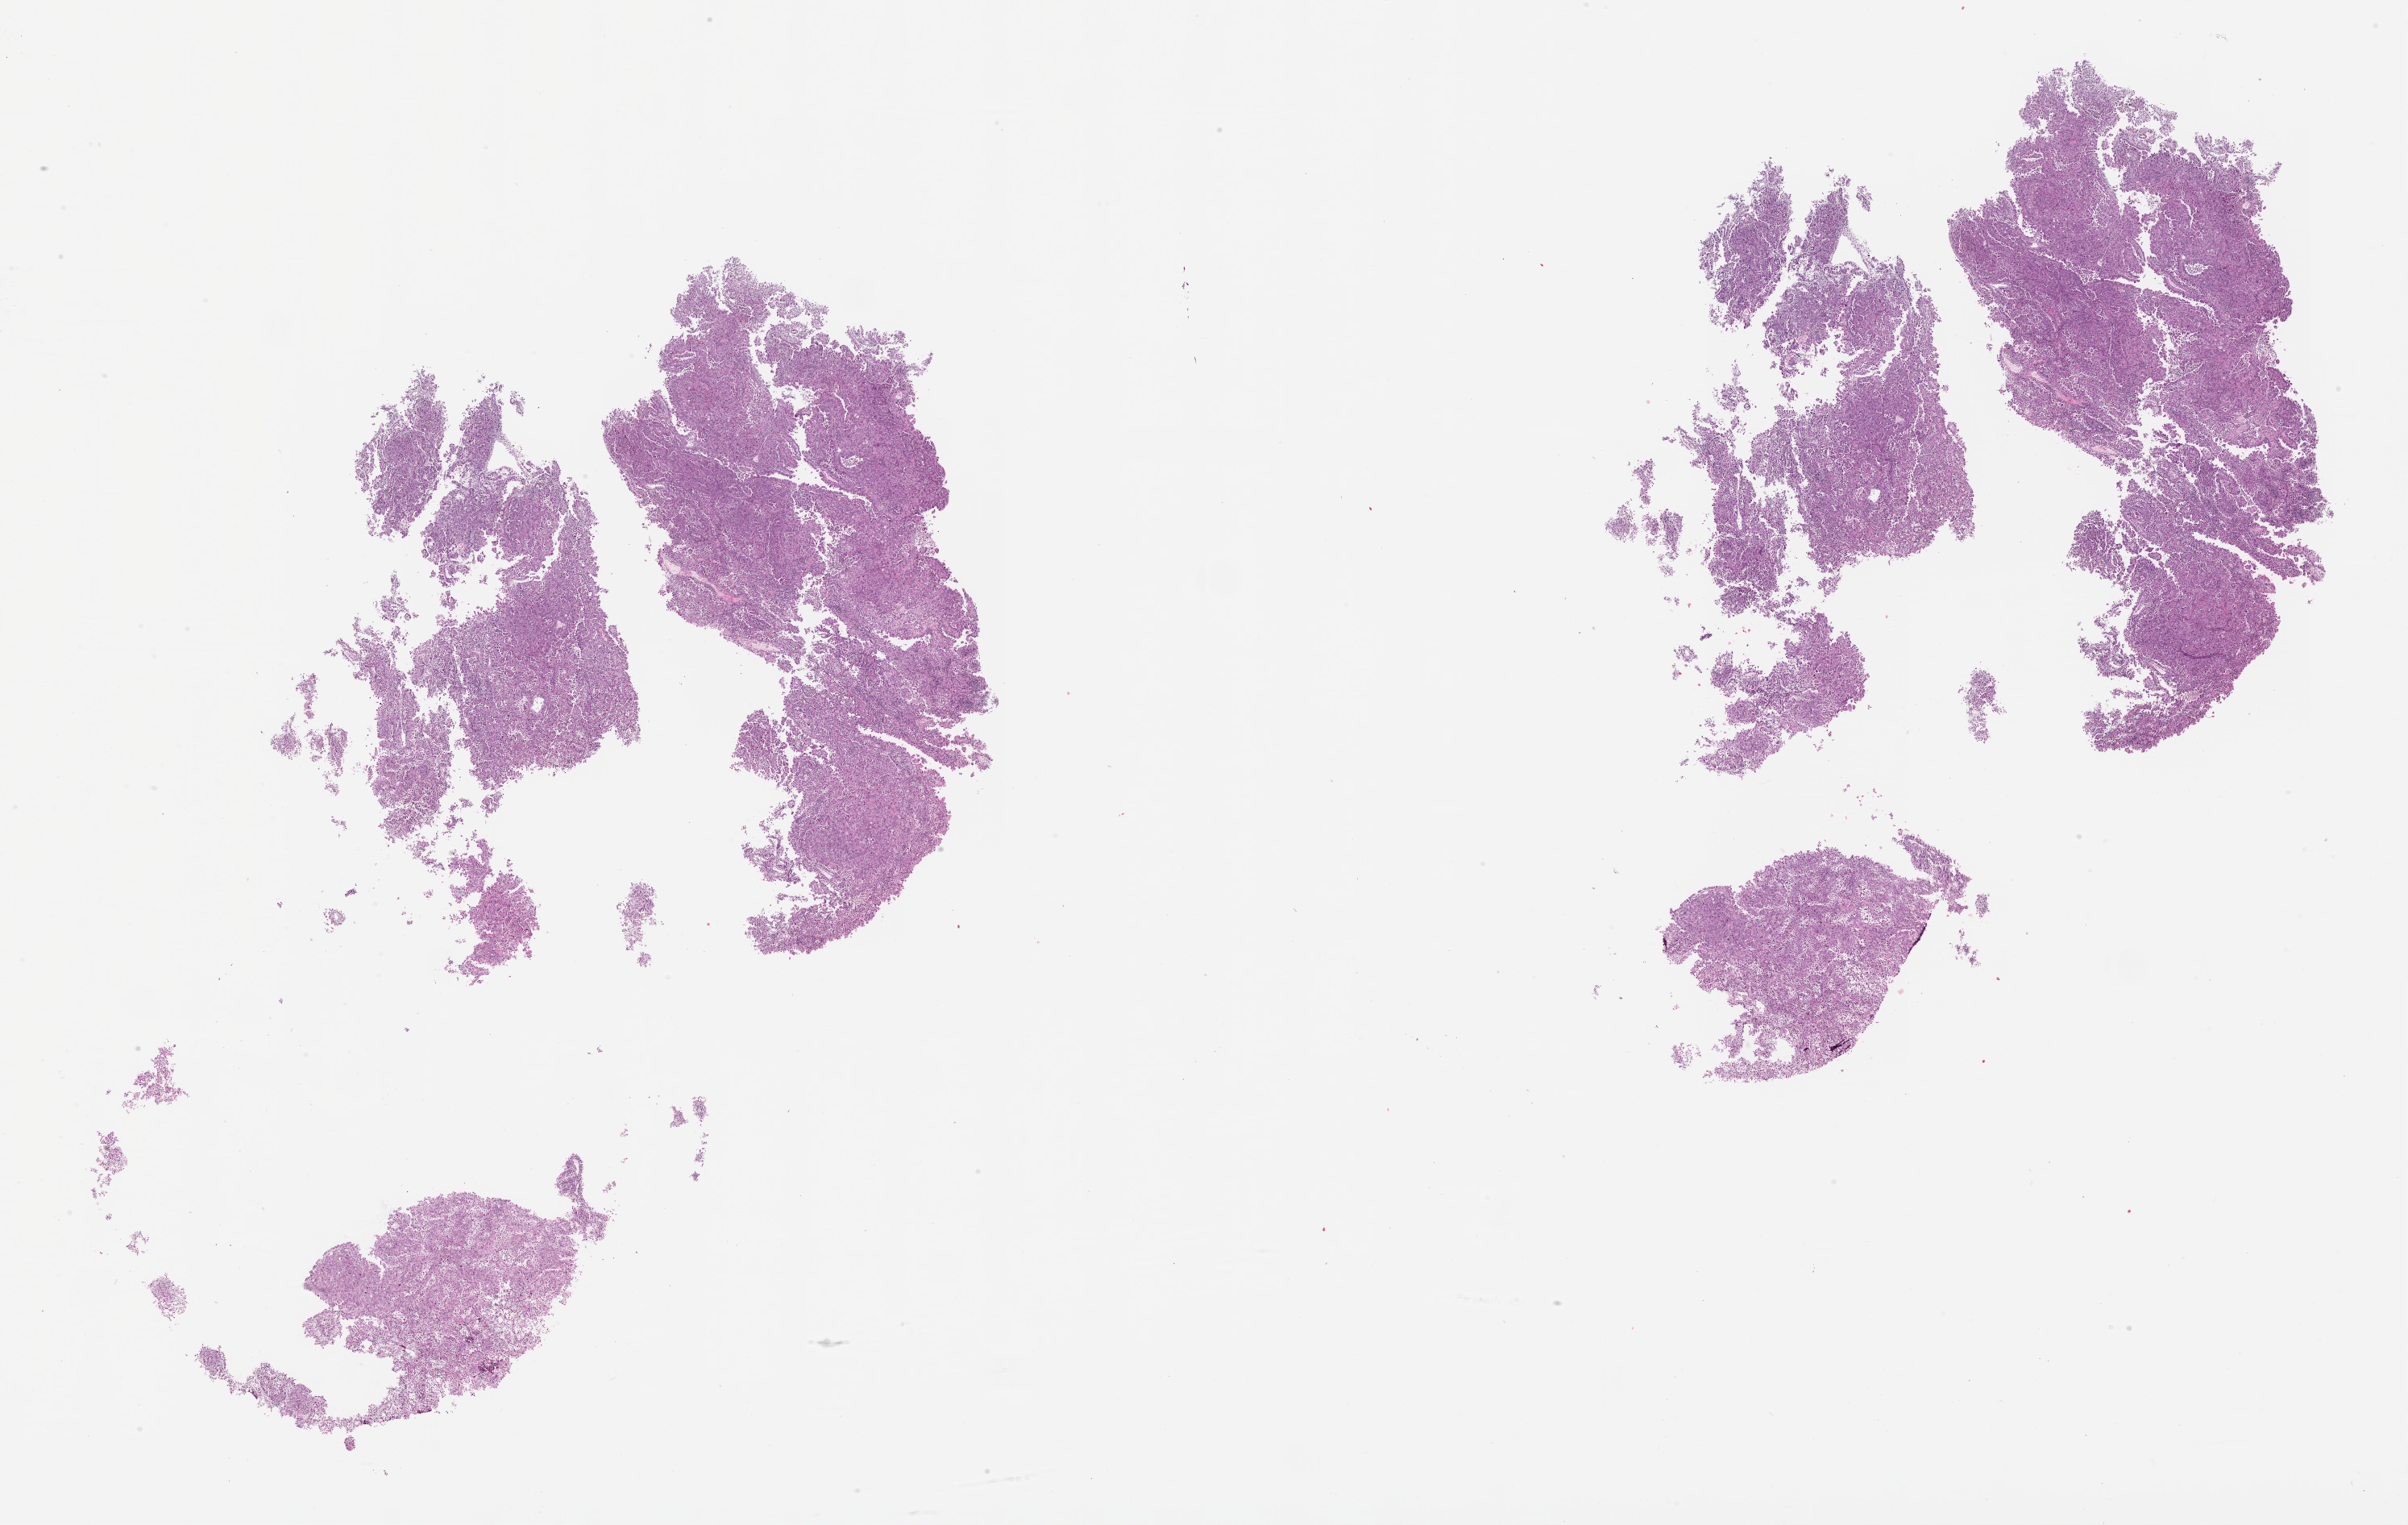
Digitized H&E-stained tissue section (whole slide) — shown as a low-resolution overview of the whole scanned area (about 24.1 x 15.2 mm); uterus, tissue type not recorded.
* patient diagnosis (cohort enrolment): corpus endometrial carcinoma (uterus)